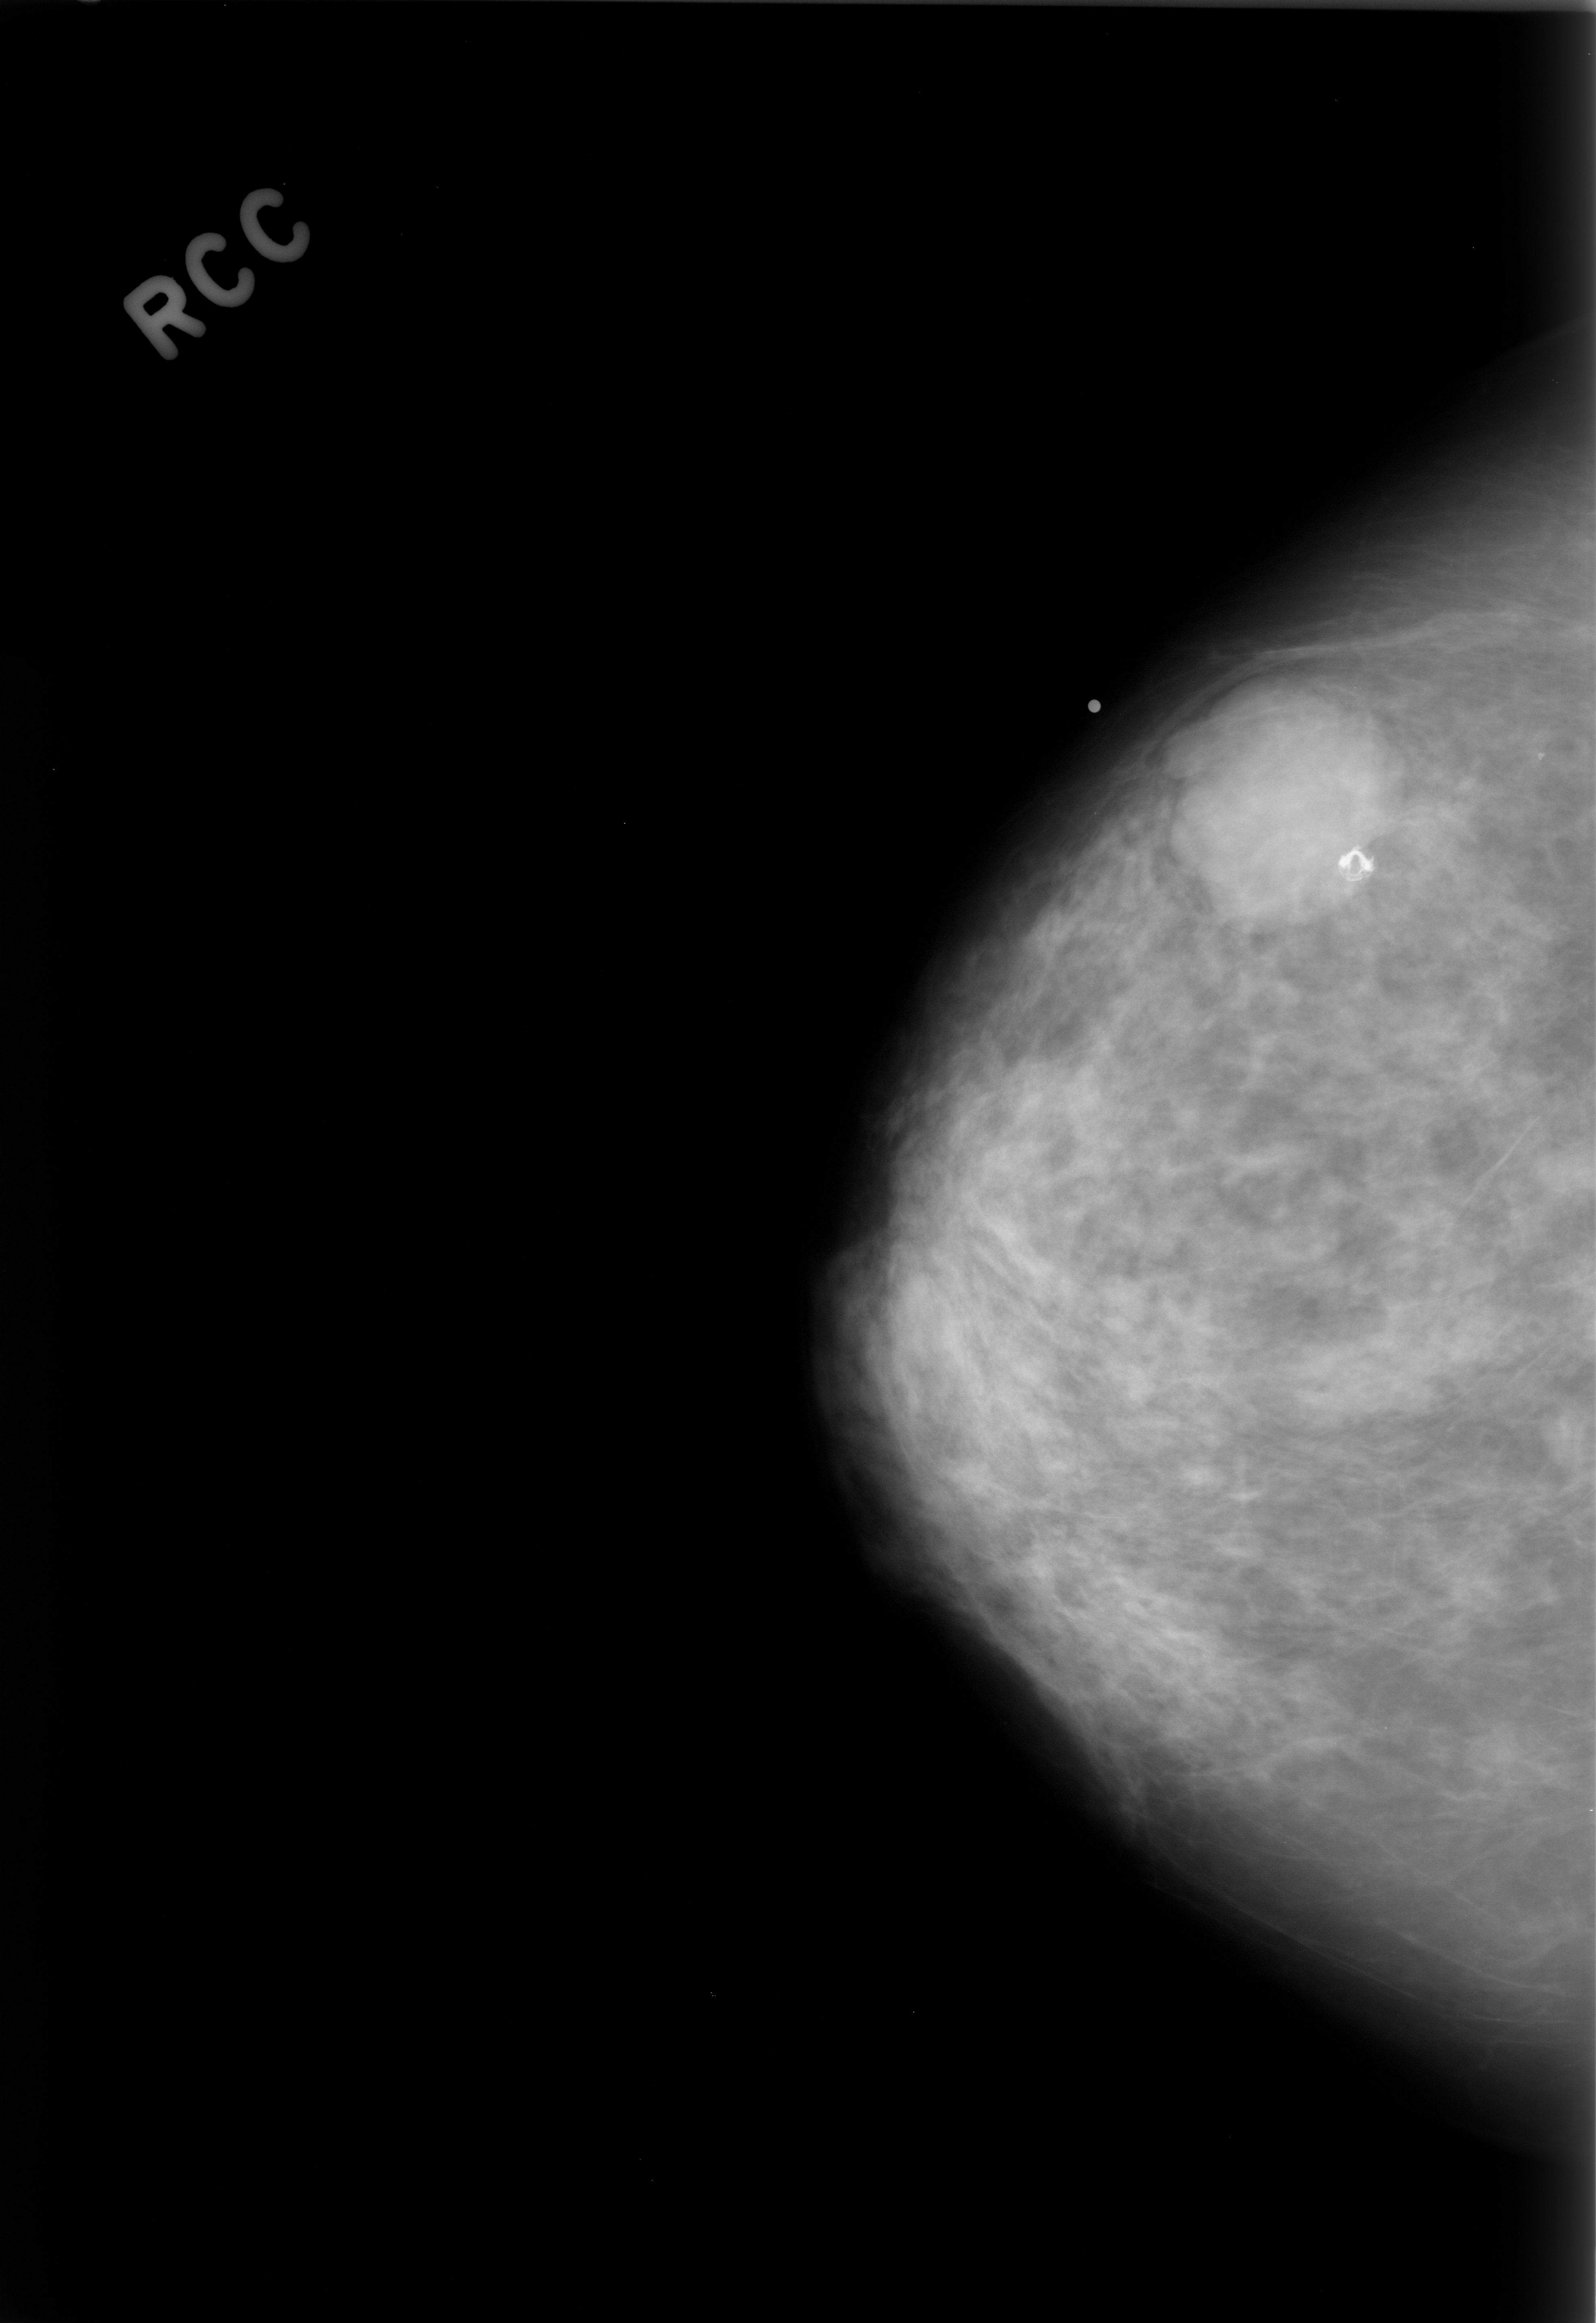
Digitized screen-film mammogram; right breast; craniocaudal (CC) view; BI-RADS breast density category 2 (scale 1–4); 1596 × 2323 image matrix.
Expert-marked regions of interest on this image (one box per marked abnormality):
- mass, shape round, margins microlobulated; BI-RADS assessment category 4; pathology result (as recorded, not read from the image): benign: bounding box (x1, y1, x2, y2) in pixels: (1171, 676, 1376, 903)